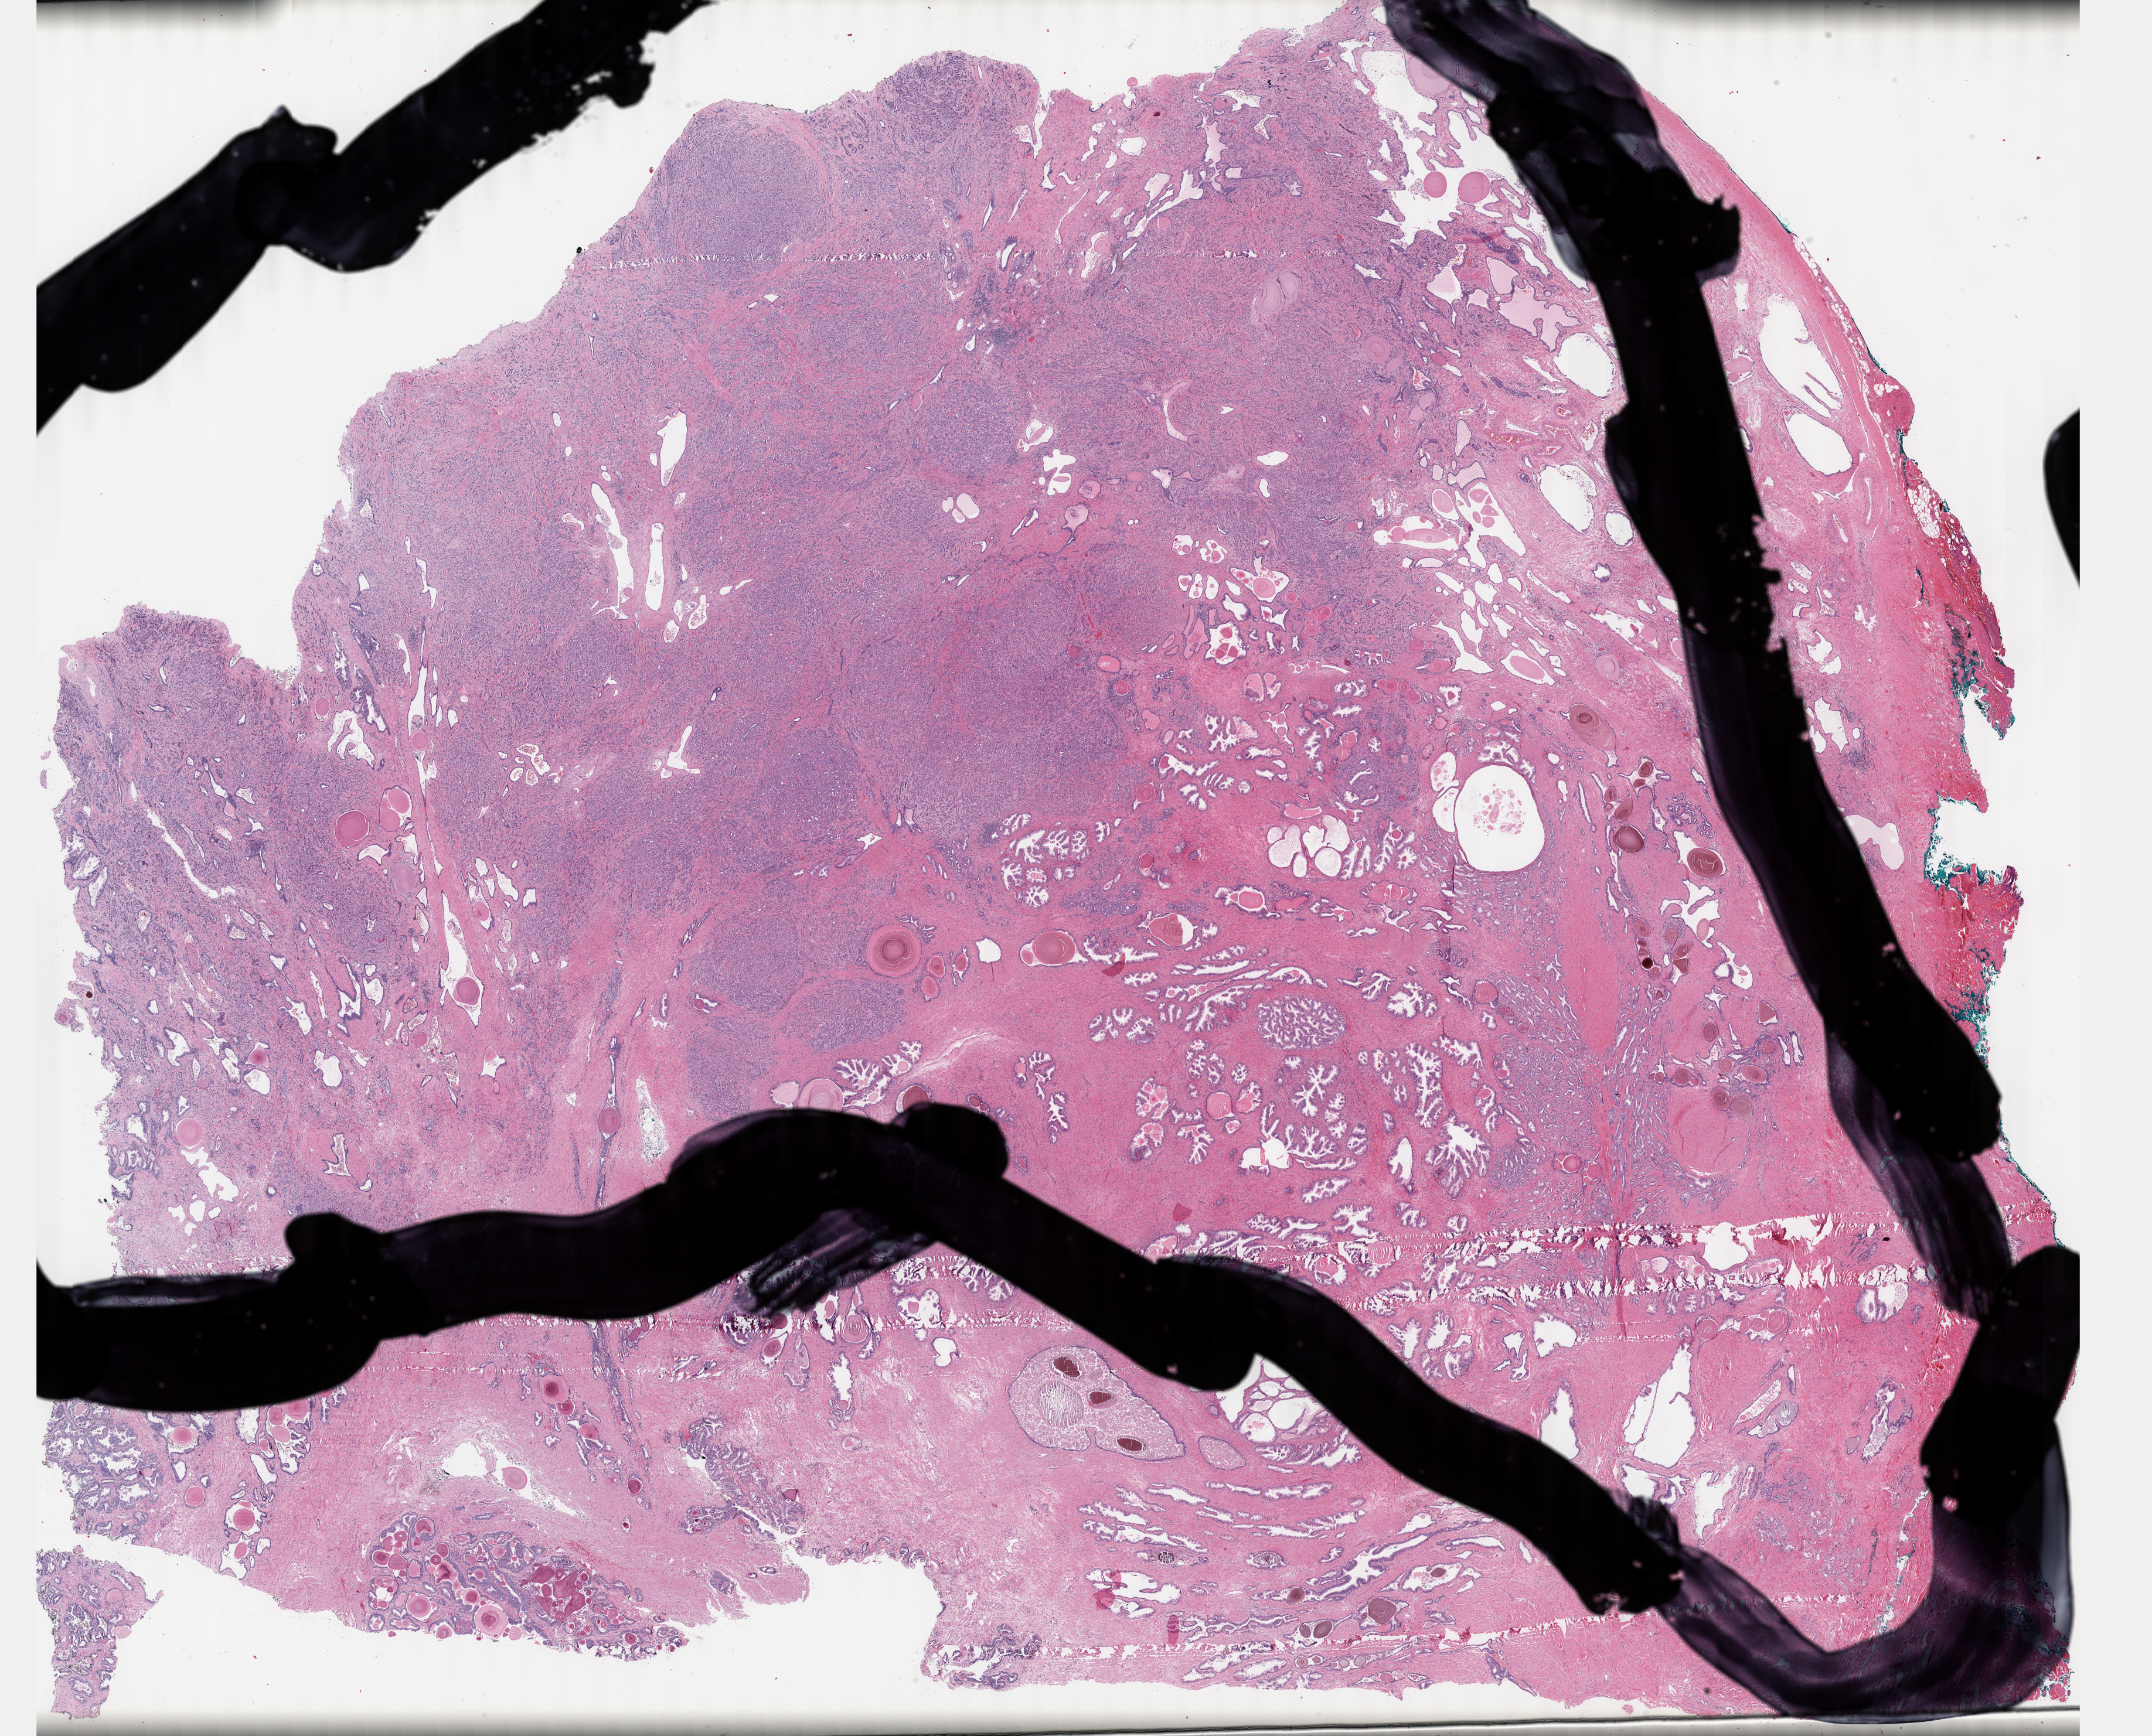
H&E whole-slide image — a low-resolution overview of the entire scanned area, about 29.2 x 23.6 mm (acquisition: 40x scan). Formalin-fixed paraffin-embedded (FFPE) diagnostic section. Prostate, primary tumour sample. Patient: male, age at initial diagnosis 62 years. Gleason score: 8 (4+4).
Diagnosis: Adenocarcinoma, NOS (prostate gland). Lymph nodes positive (case pathology): 0 of 2 examined.